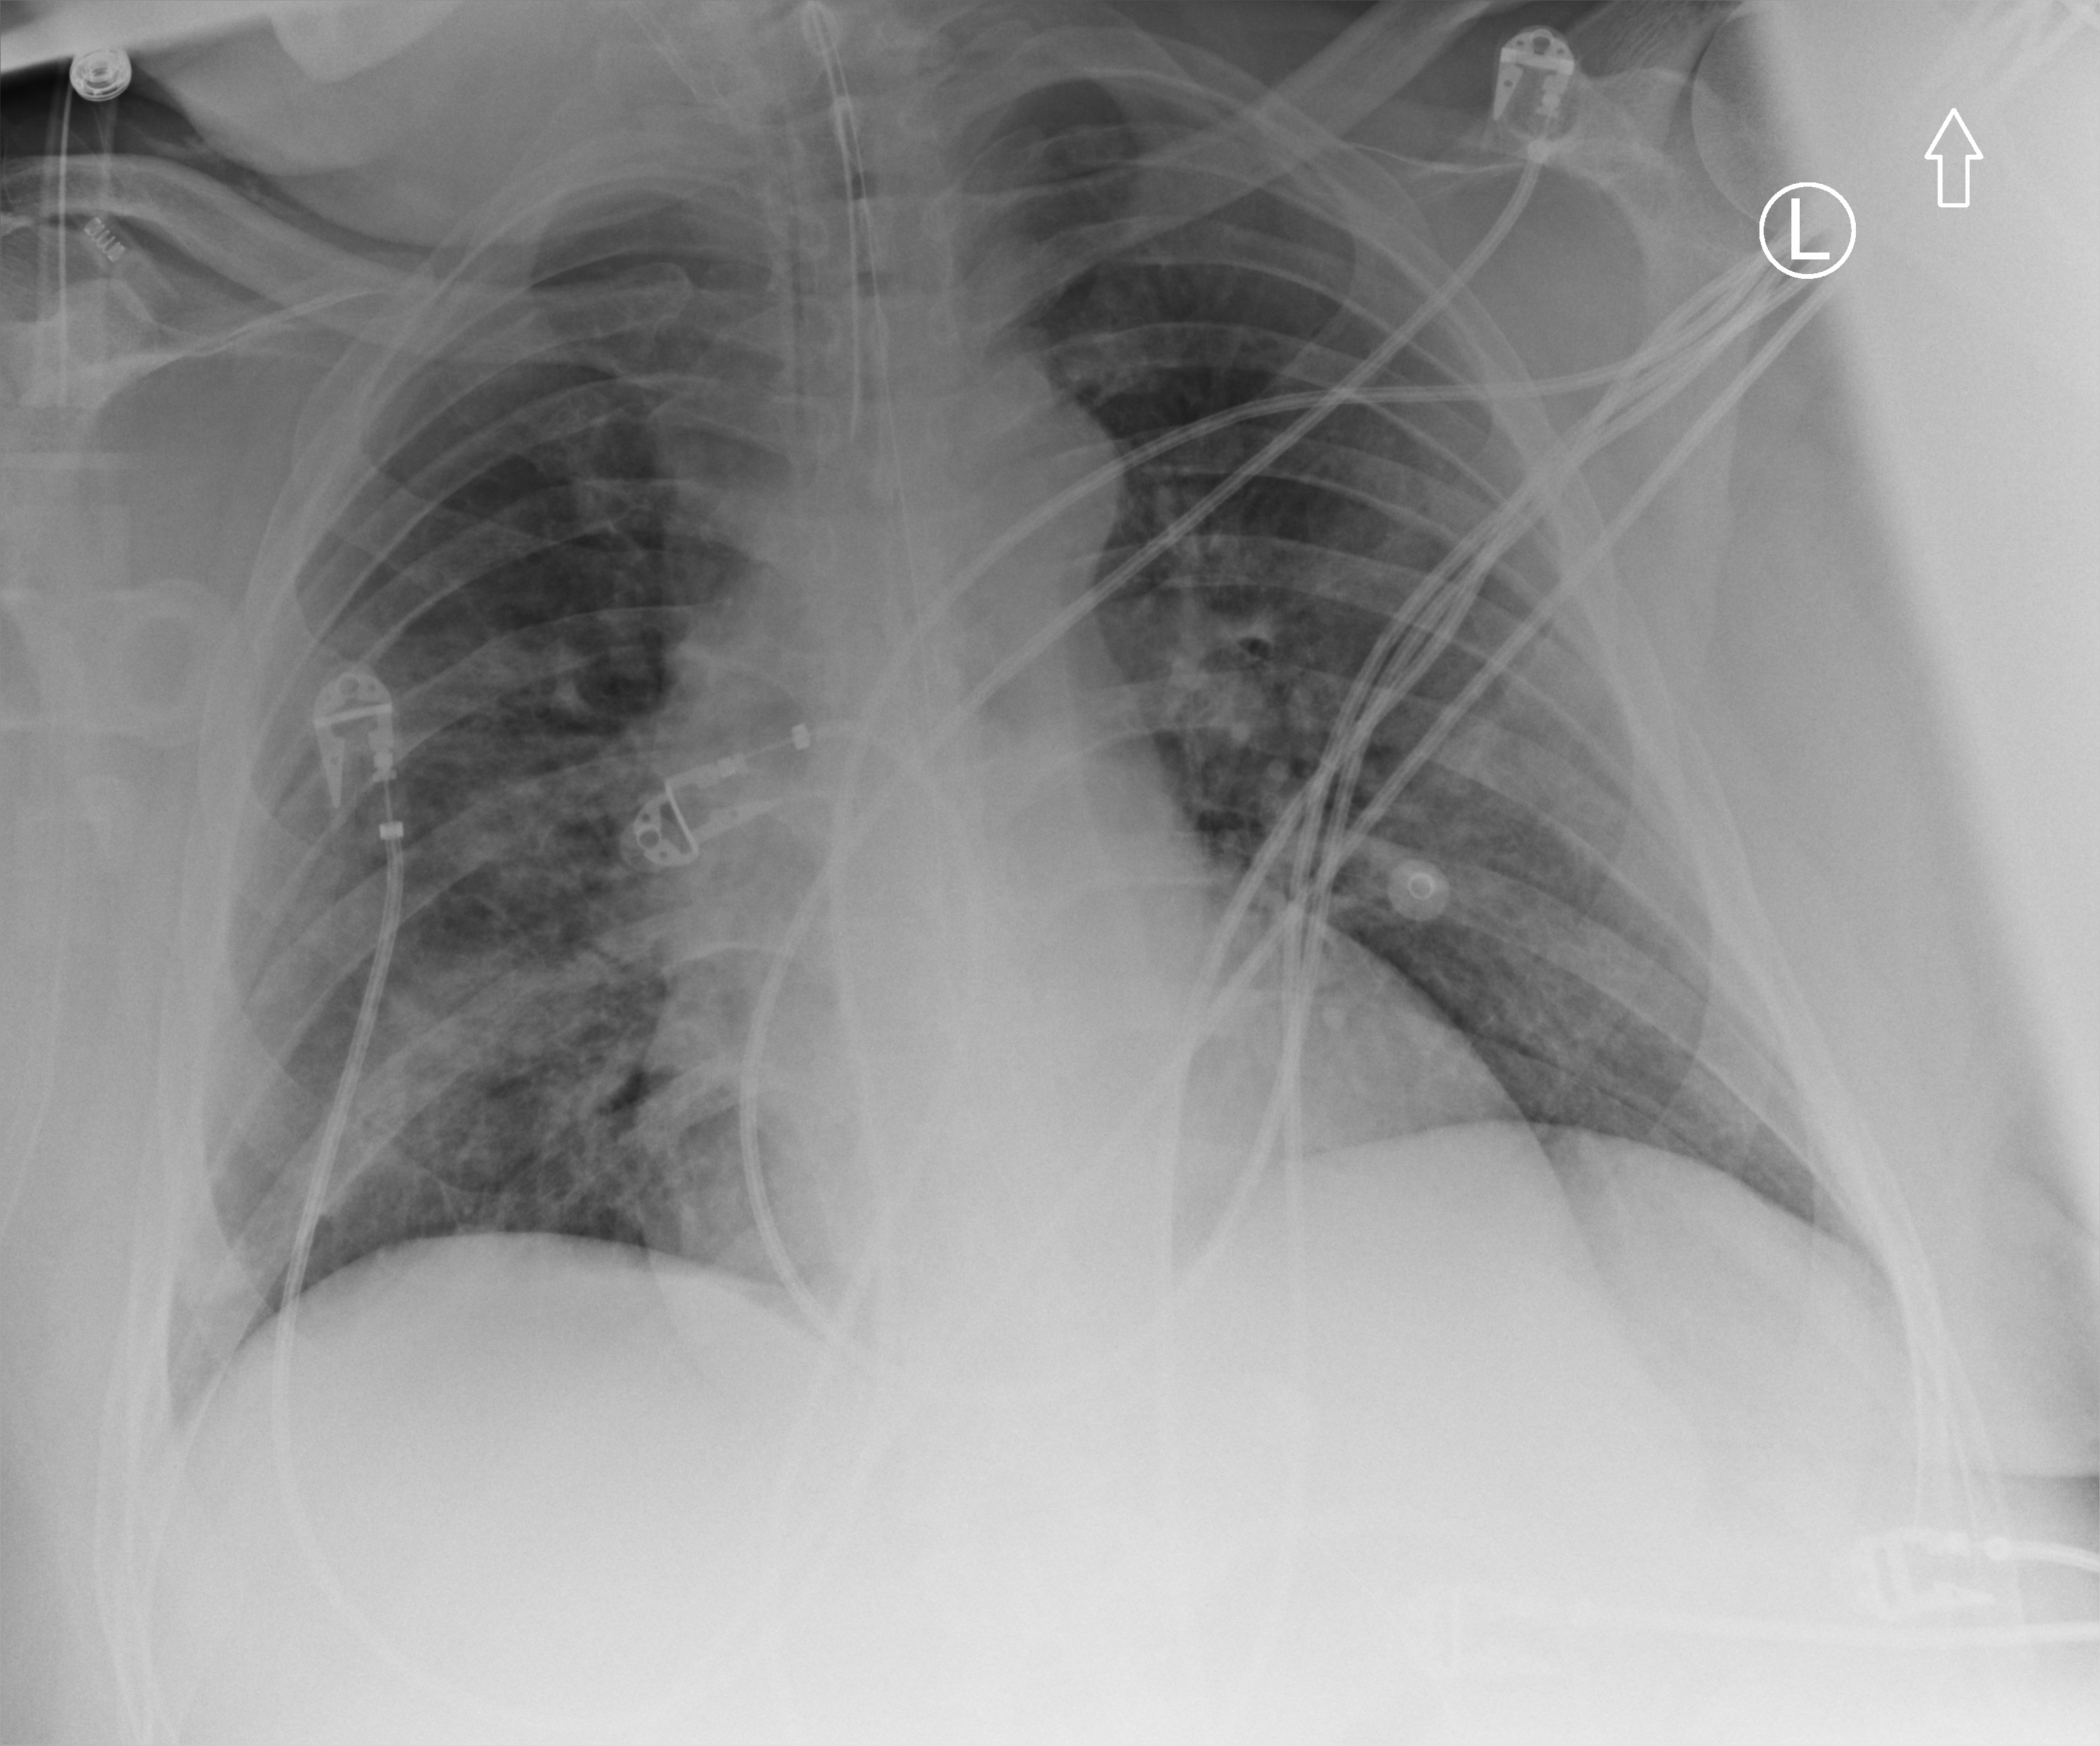
Bedside chest radiograph (computed radiography). Male patient hospitalised with COVID-19, age 60–74 years.
From the hospital-stay record, not from the radiograph (when in the stay this image was taken is not recorded):
- mechanically ventilated during this hospital stay: yes